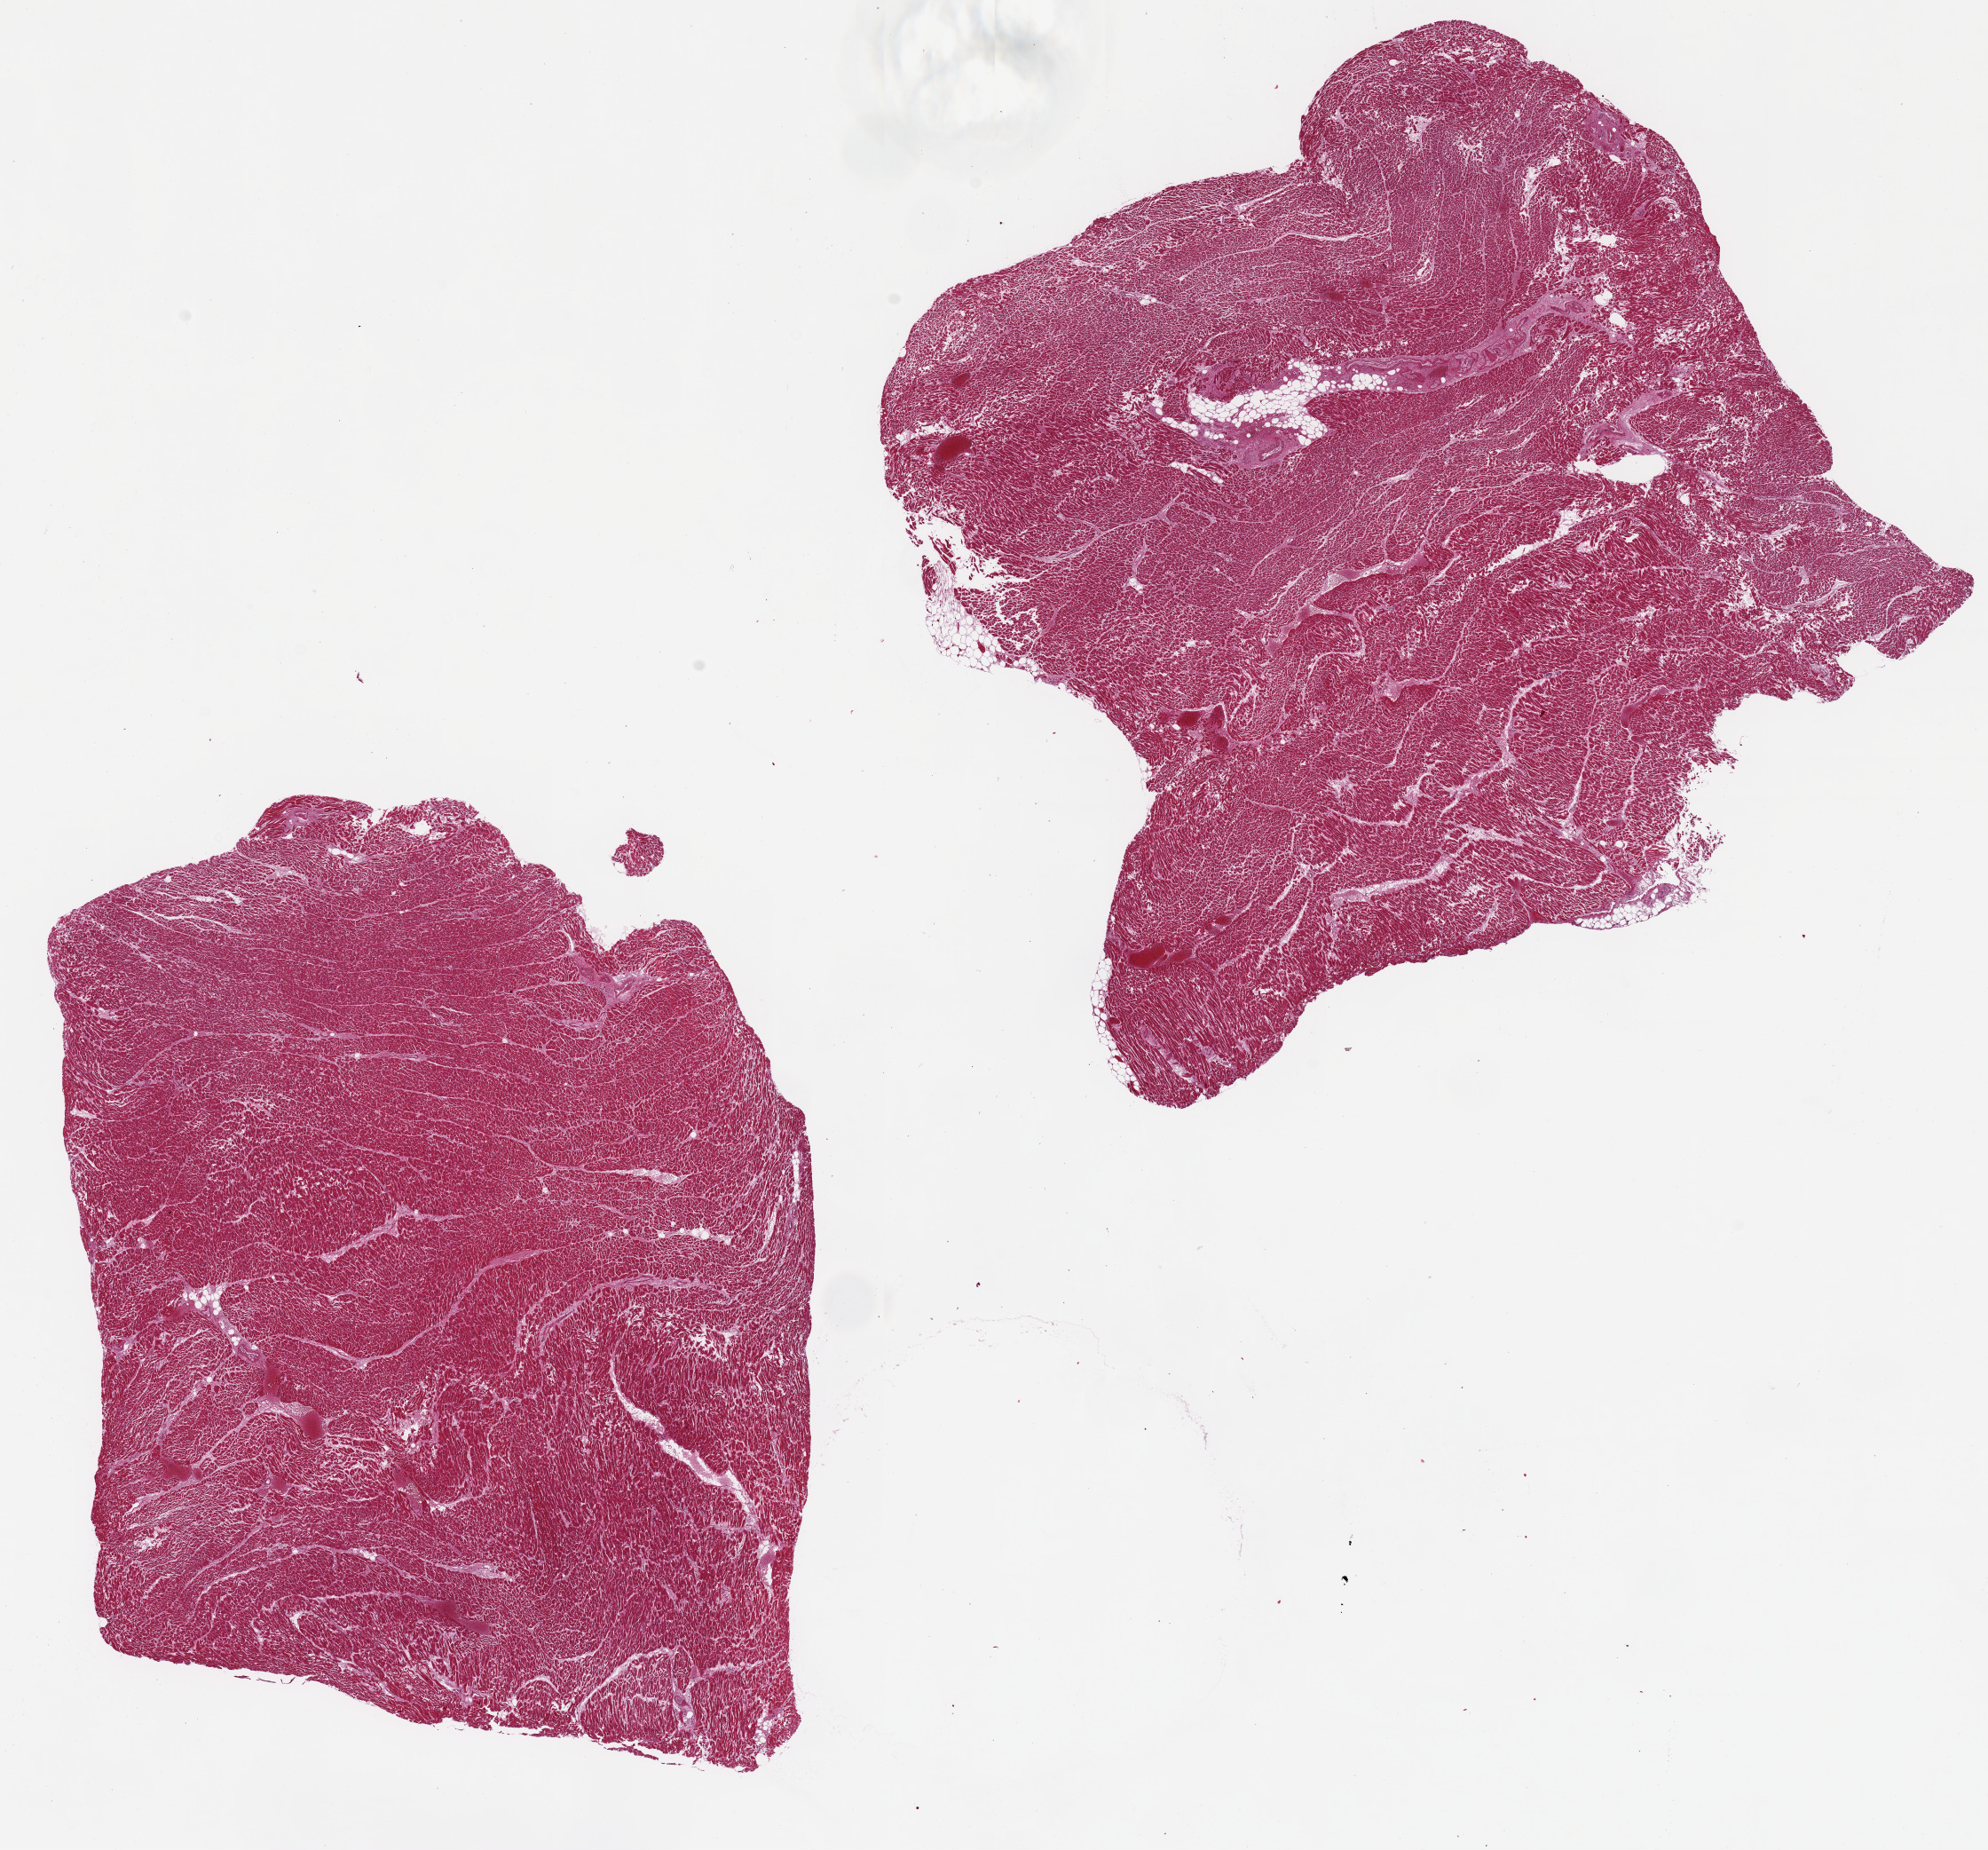
Hematoxylin and eosin (H&E) whole-slide image, whole scanned area (about 17.7 x 16.5 mm) shown as a low-resolution overview. PAXgene-fixed paraffin-embedded (PFPE) section. Sampled site (target tissue): heart. Donor tissue sample. Donor sex: female.
* review note (as recorded): 2 pieces, 9x6 & 9x8mm; minimal interstitial fibrosis